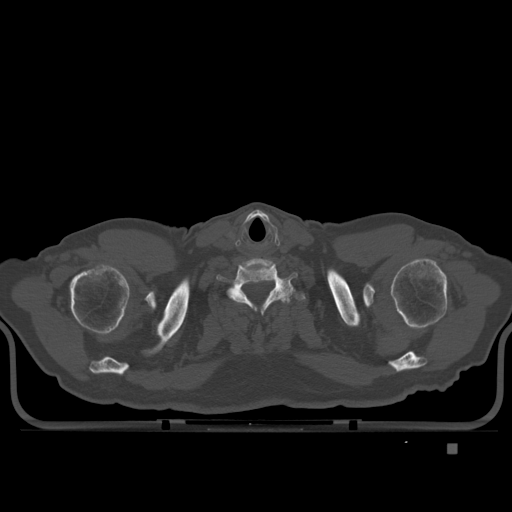
CT including the spine, one axial slice. Position 332 of 435 along the scan axis. Bone window (W 1800 / L 400 HU). 1.5 mm slice thickness. 512 × 512 image matrix, field of view 434 × 434 mm. Patient: male, 73 years. Case-level facts recorded for this patient, not image findings: primary cancer: skin.
Outlined on this slice (semi-automatically segmented with operator editing):
- T1 vertebra: bounding box <213,285,302,345> (left, top, right, bottom; pixels)